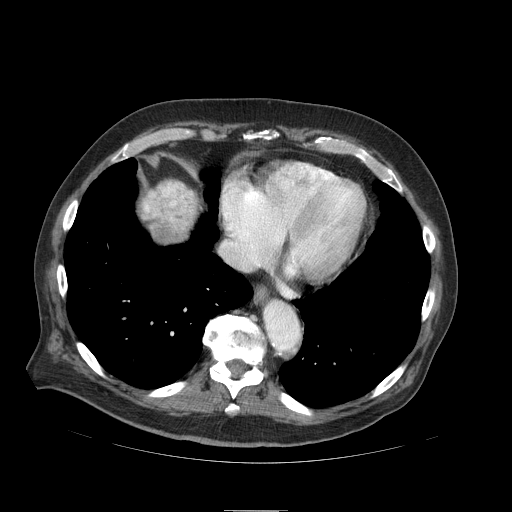
Contrast-enhanced abdominal CT (liver protocol), one axial slice. Position 86 of 103 along the scan axis. Soft-tissue window (W 400 / L 40 HU). 512 × 512 image matrix, field of view 440 × 440 mm. From the clinical record (not read from this slice): diagnosis: hepatocellular carcinoma (patient treated with transarterial chemoembolisation; whether this scan precedes or follows treatment is not stated here); TNM stage (as recorded): Stage-IIIA; Child-Pugh class: B.
Structures marked on this image (semi-automatically segmented with operator editing):
- liver parenchyma outside the tumour (the mass and vessels are separate outlines, so this box may not span the whole liver): box from (x=196, y=203) to (x=198, y=210) px
- mass: (x=138, y=179)–(x=199, y=243)